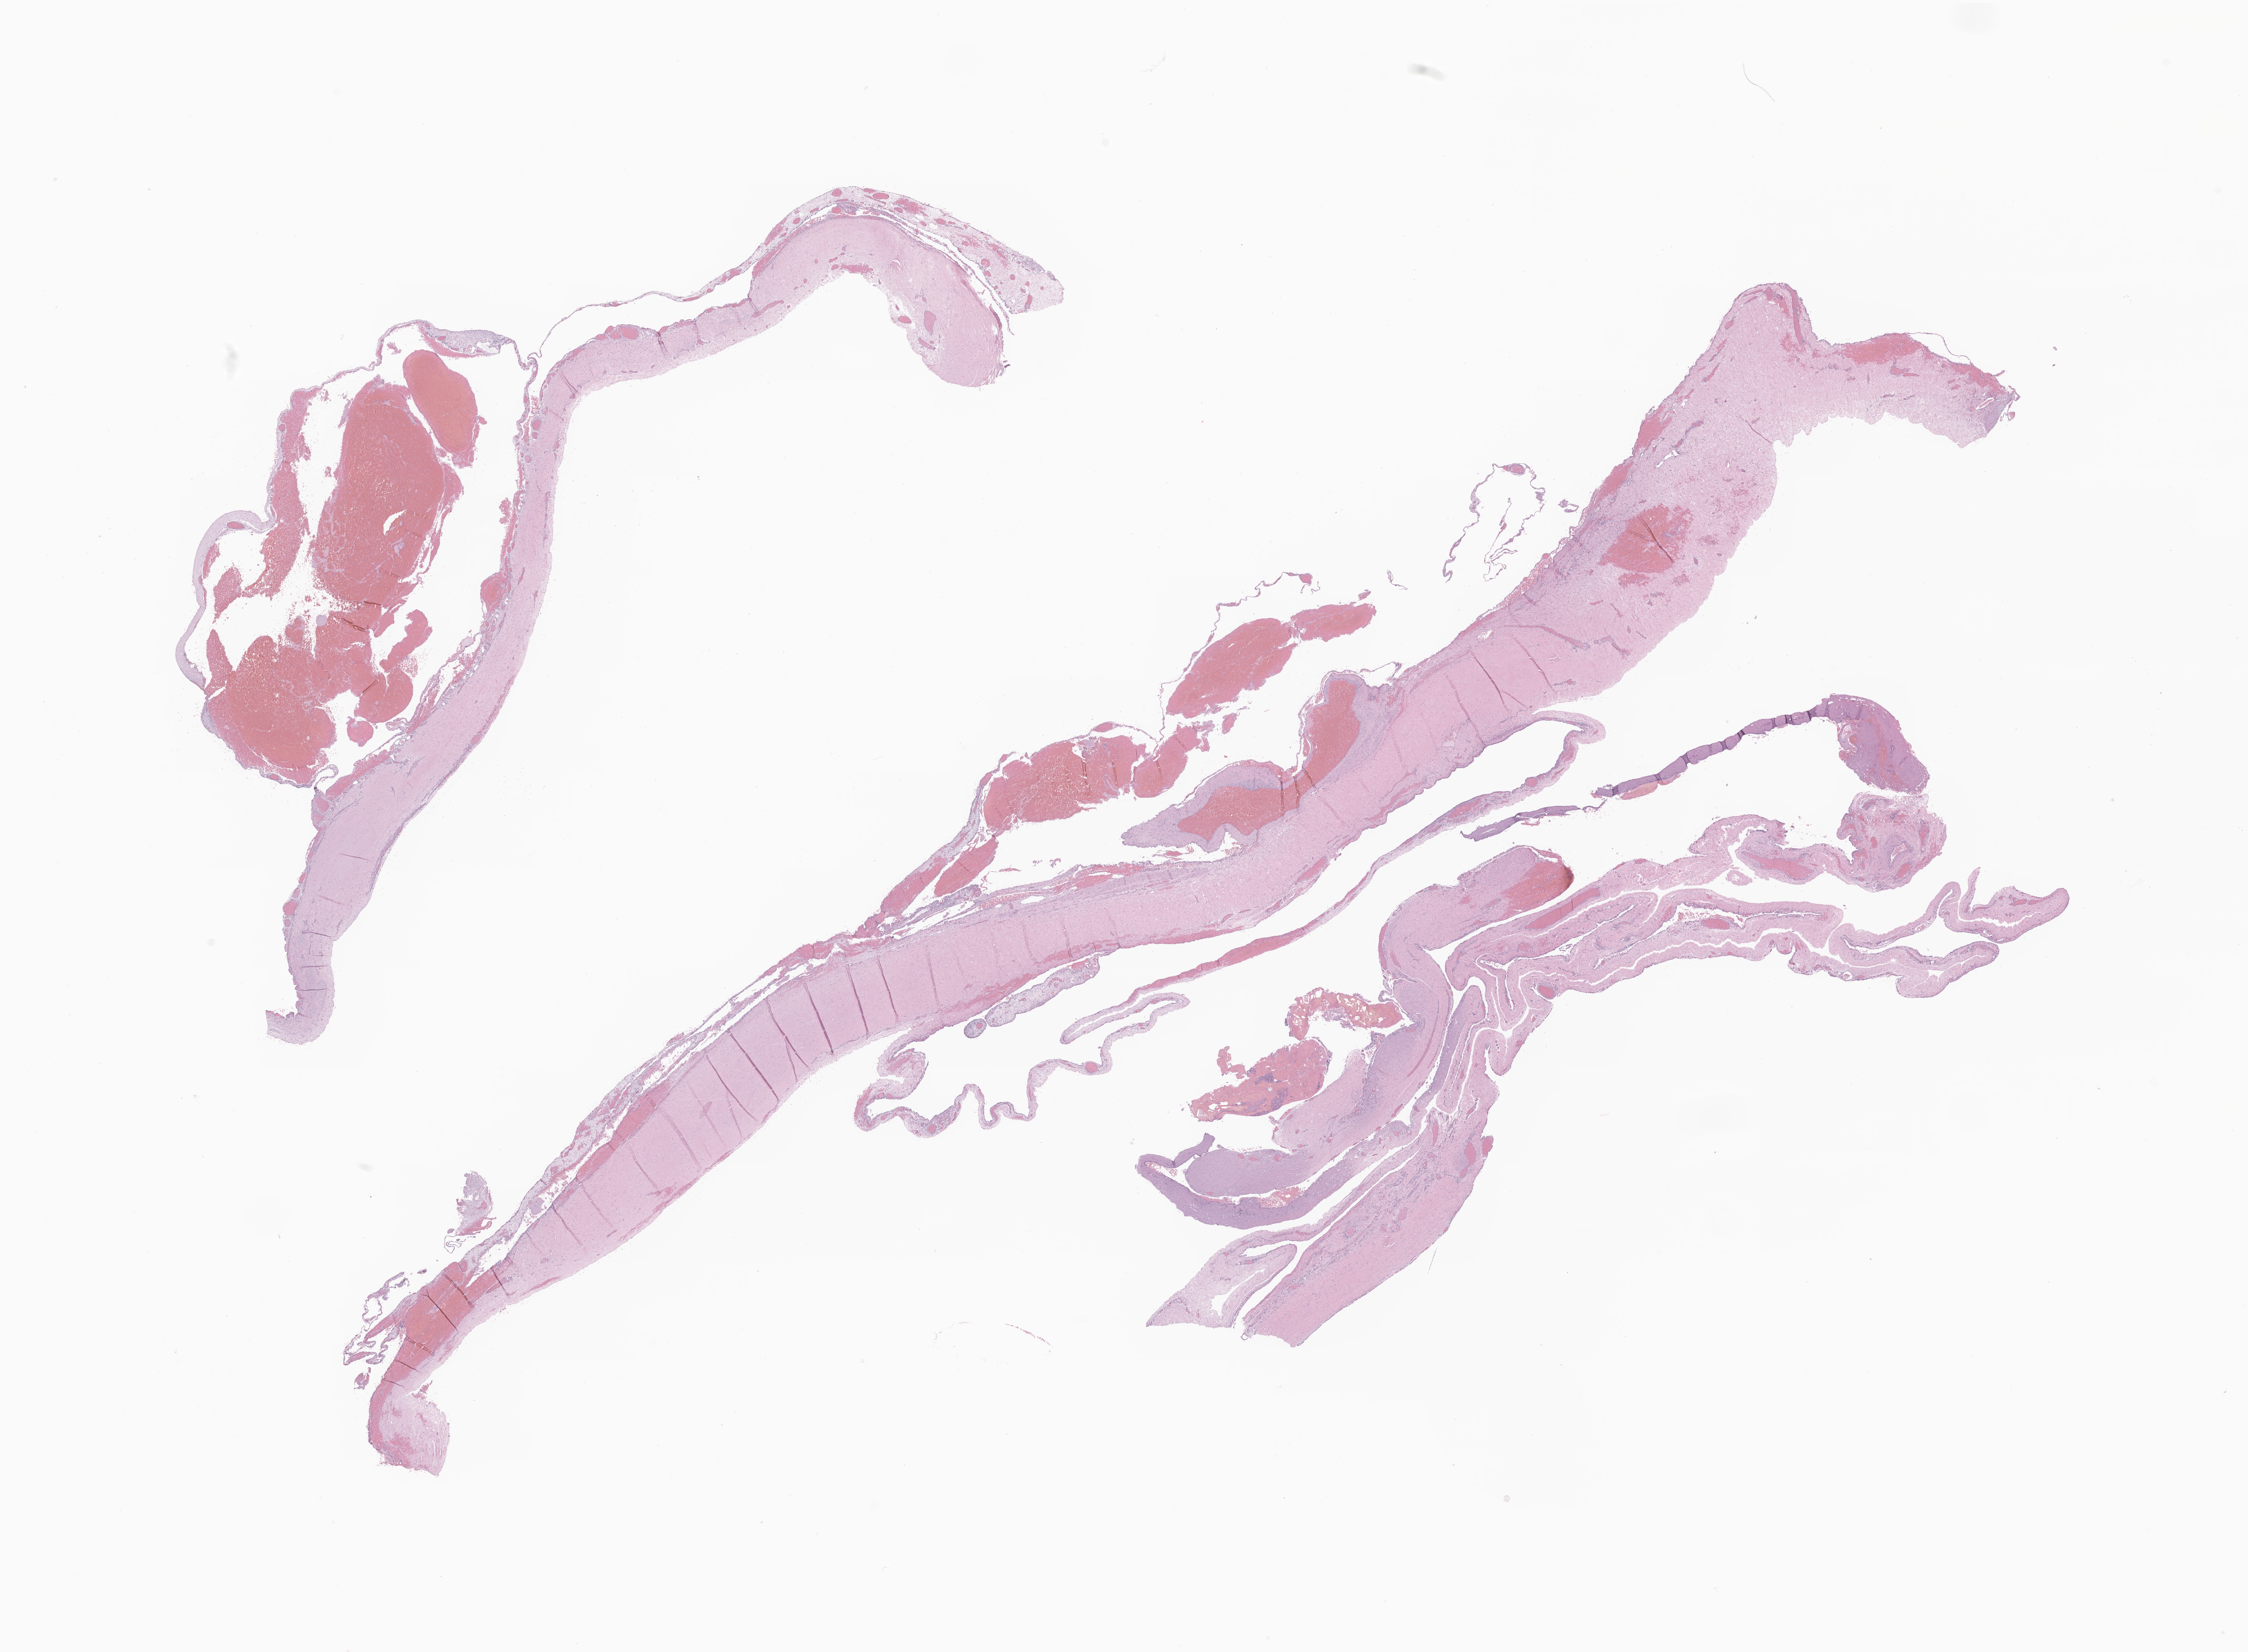
Hematoxylin and eosin (H&E) whole-slide image of tumor tissue from the upper lobe of lung, a low-resolution overview of the entire scanned area, about 24.5 x 18.0 mm, FFPE section. Male patient, age 37 months.
Recorded diagnosis: Pleuropulmonary blastoma.